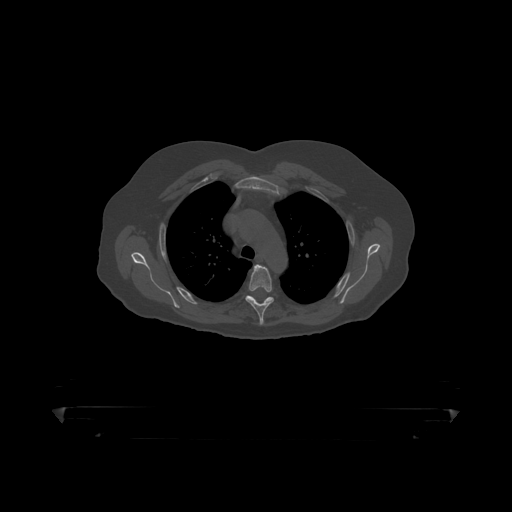
CT including the spine, one axial slice. Slice 336 of 390 in the series (ordered by position). Bone window (W 1800 / L 400 HU). 1.25 mm slice thickness. 512 × 512 image matrix, field of view 650 × 650 mm. Male patient, age 60 years. From the clinical record (not read from this slice): primary cancer: prostate.
Outlined on this slice (semi-automatic segmentation, software-assisted and operator-edited):
- T4 vertebra: box from (x=246, y=265) to (x=275, y=319) px
- T5 vertebra: (x=248, y=296)–(x=272, y=303)